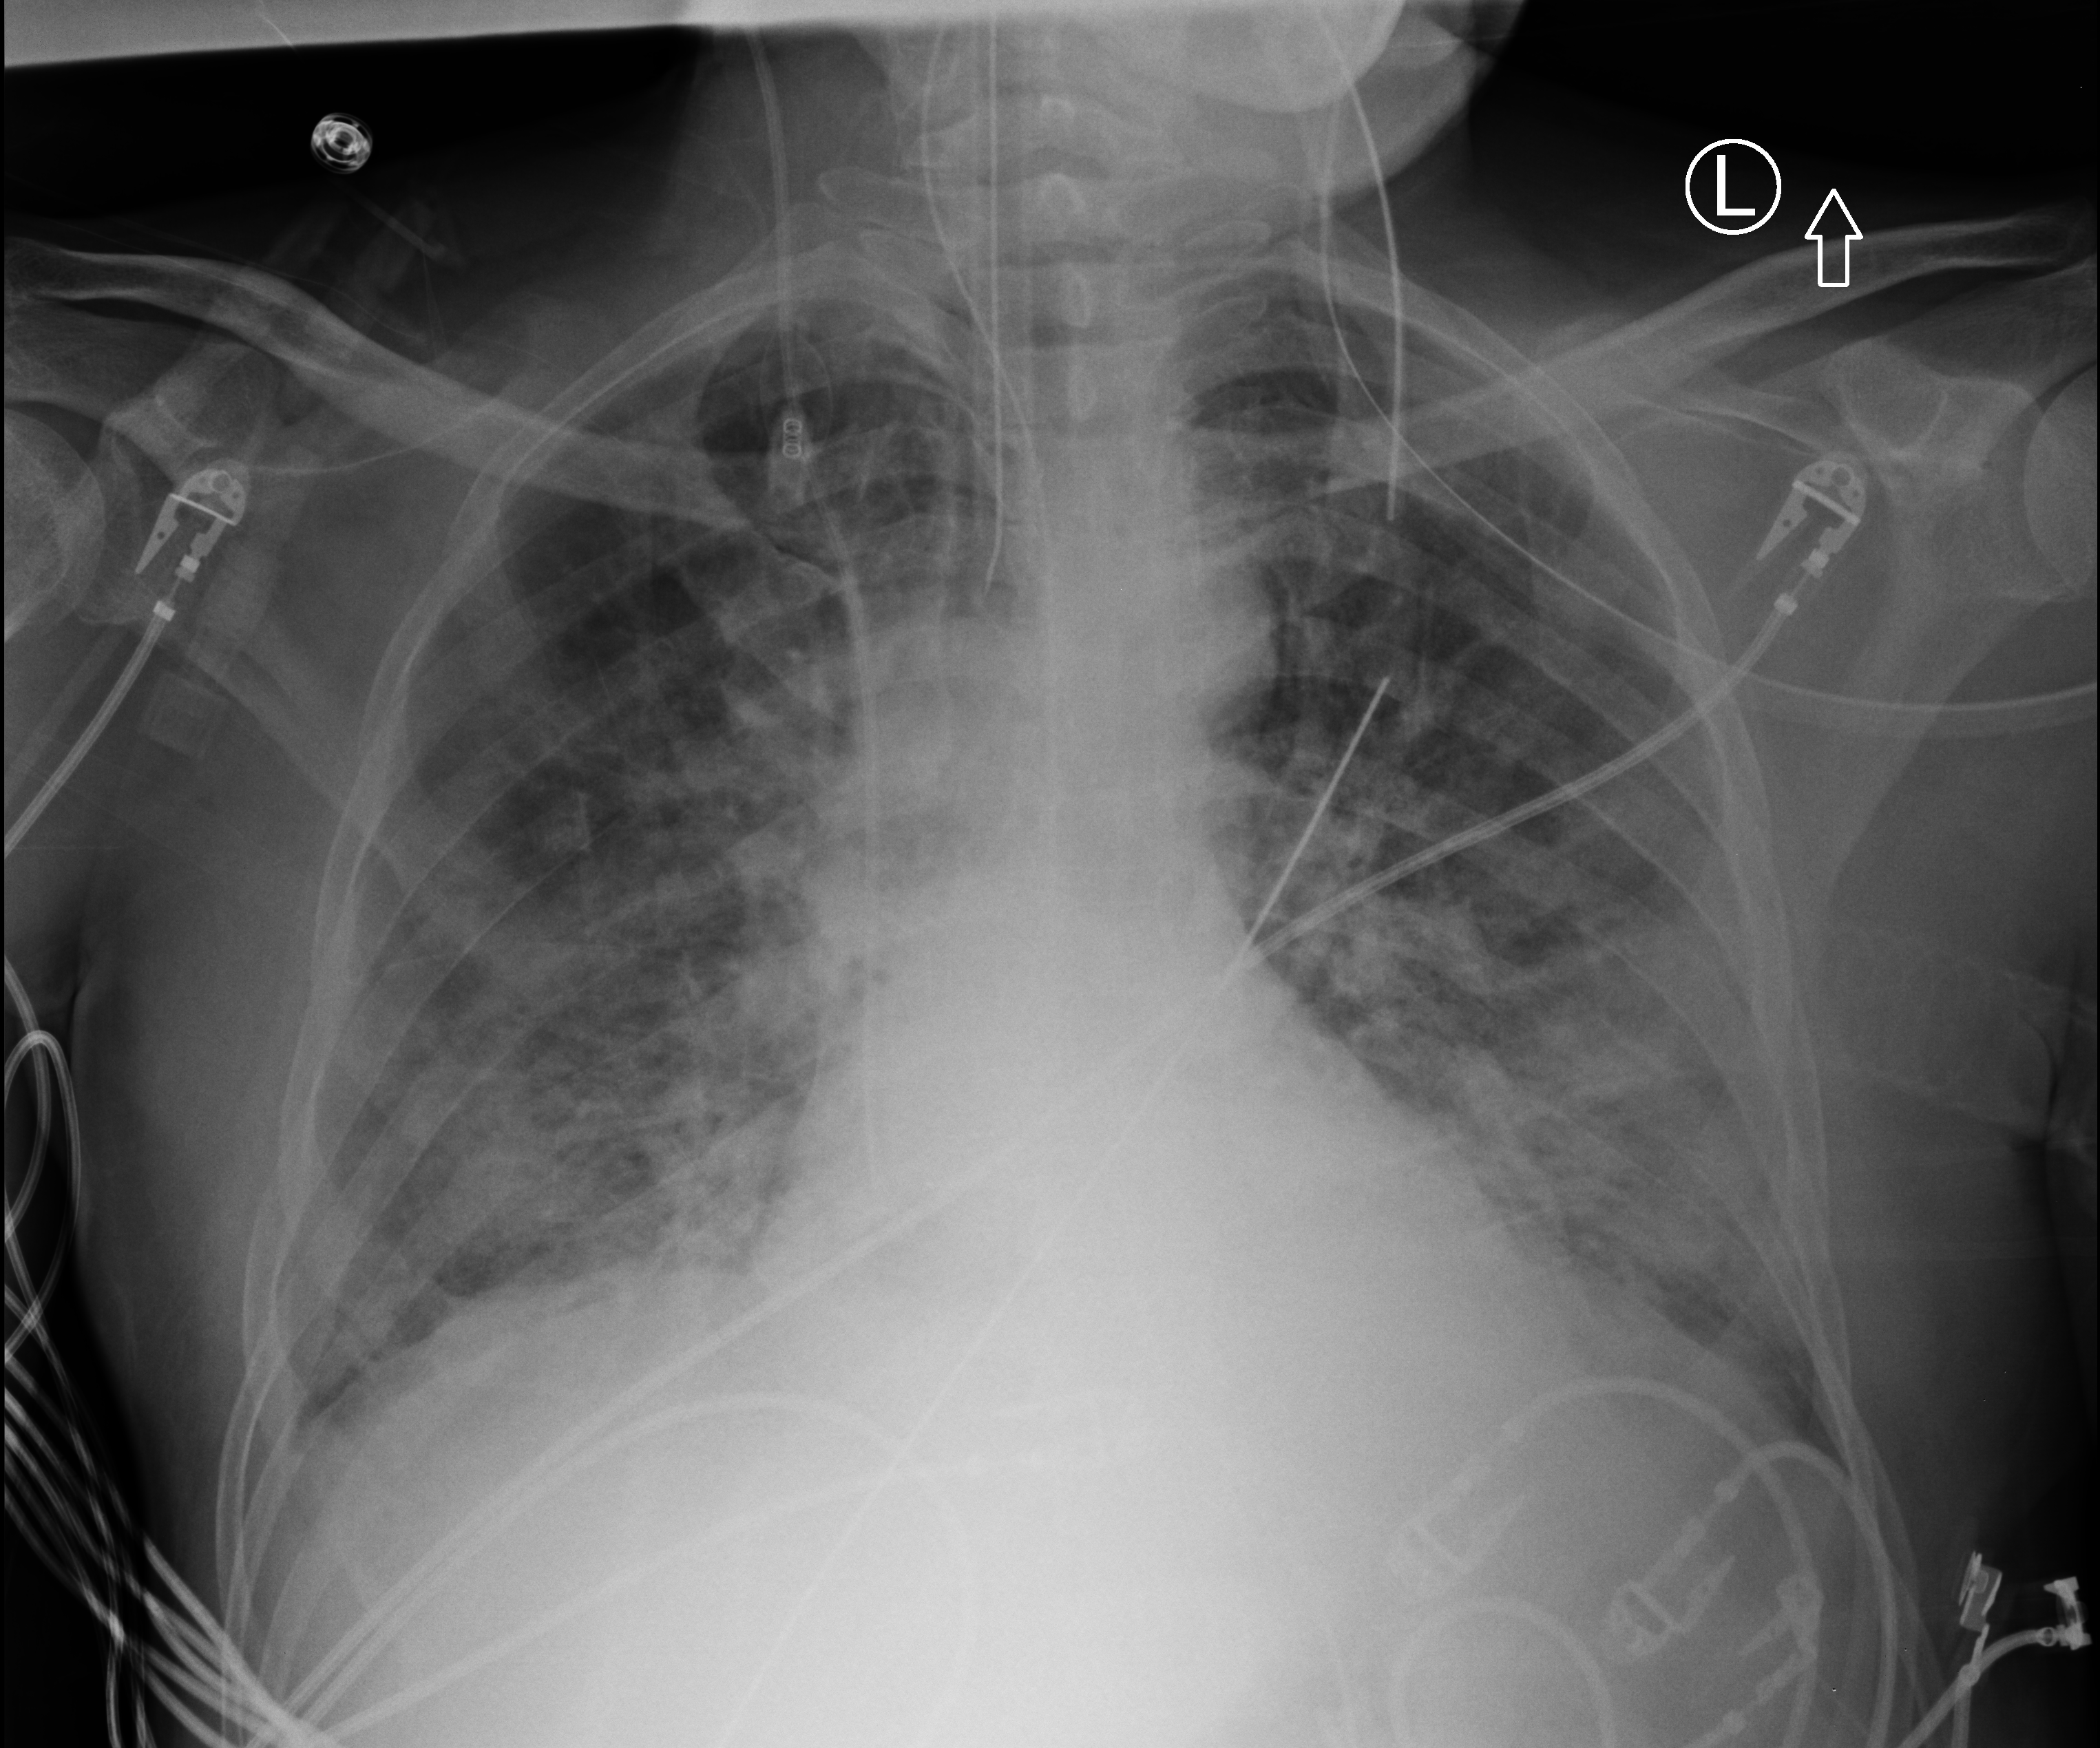
Portable chest radiograph; anteroposterior (AP) projection. Patient hospitalised with COVID-19; male, aged 18–59 years.
From the hospital-stay record, not from the radiograph (when in the stay this image was taken is not recorded): length of hospital stay: 41 days.